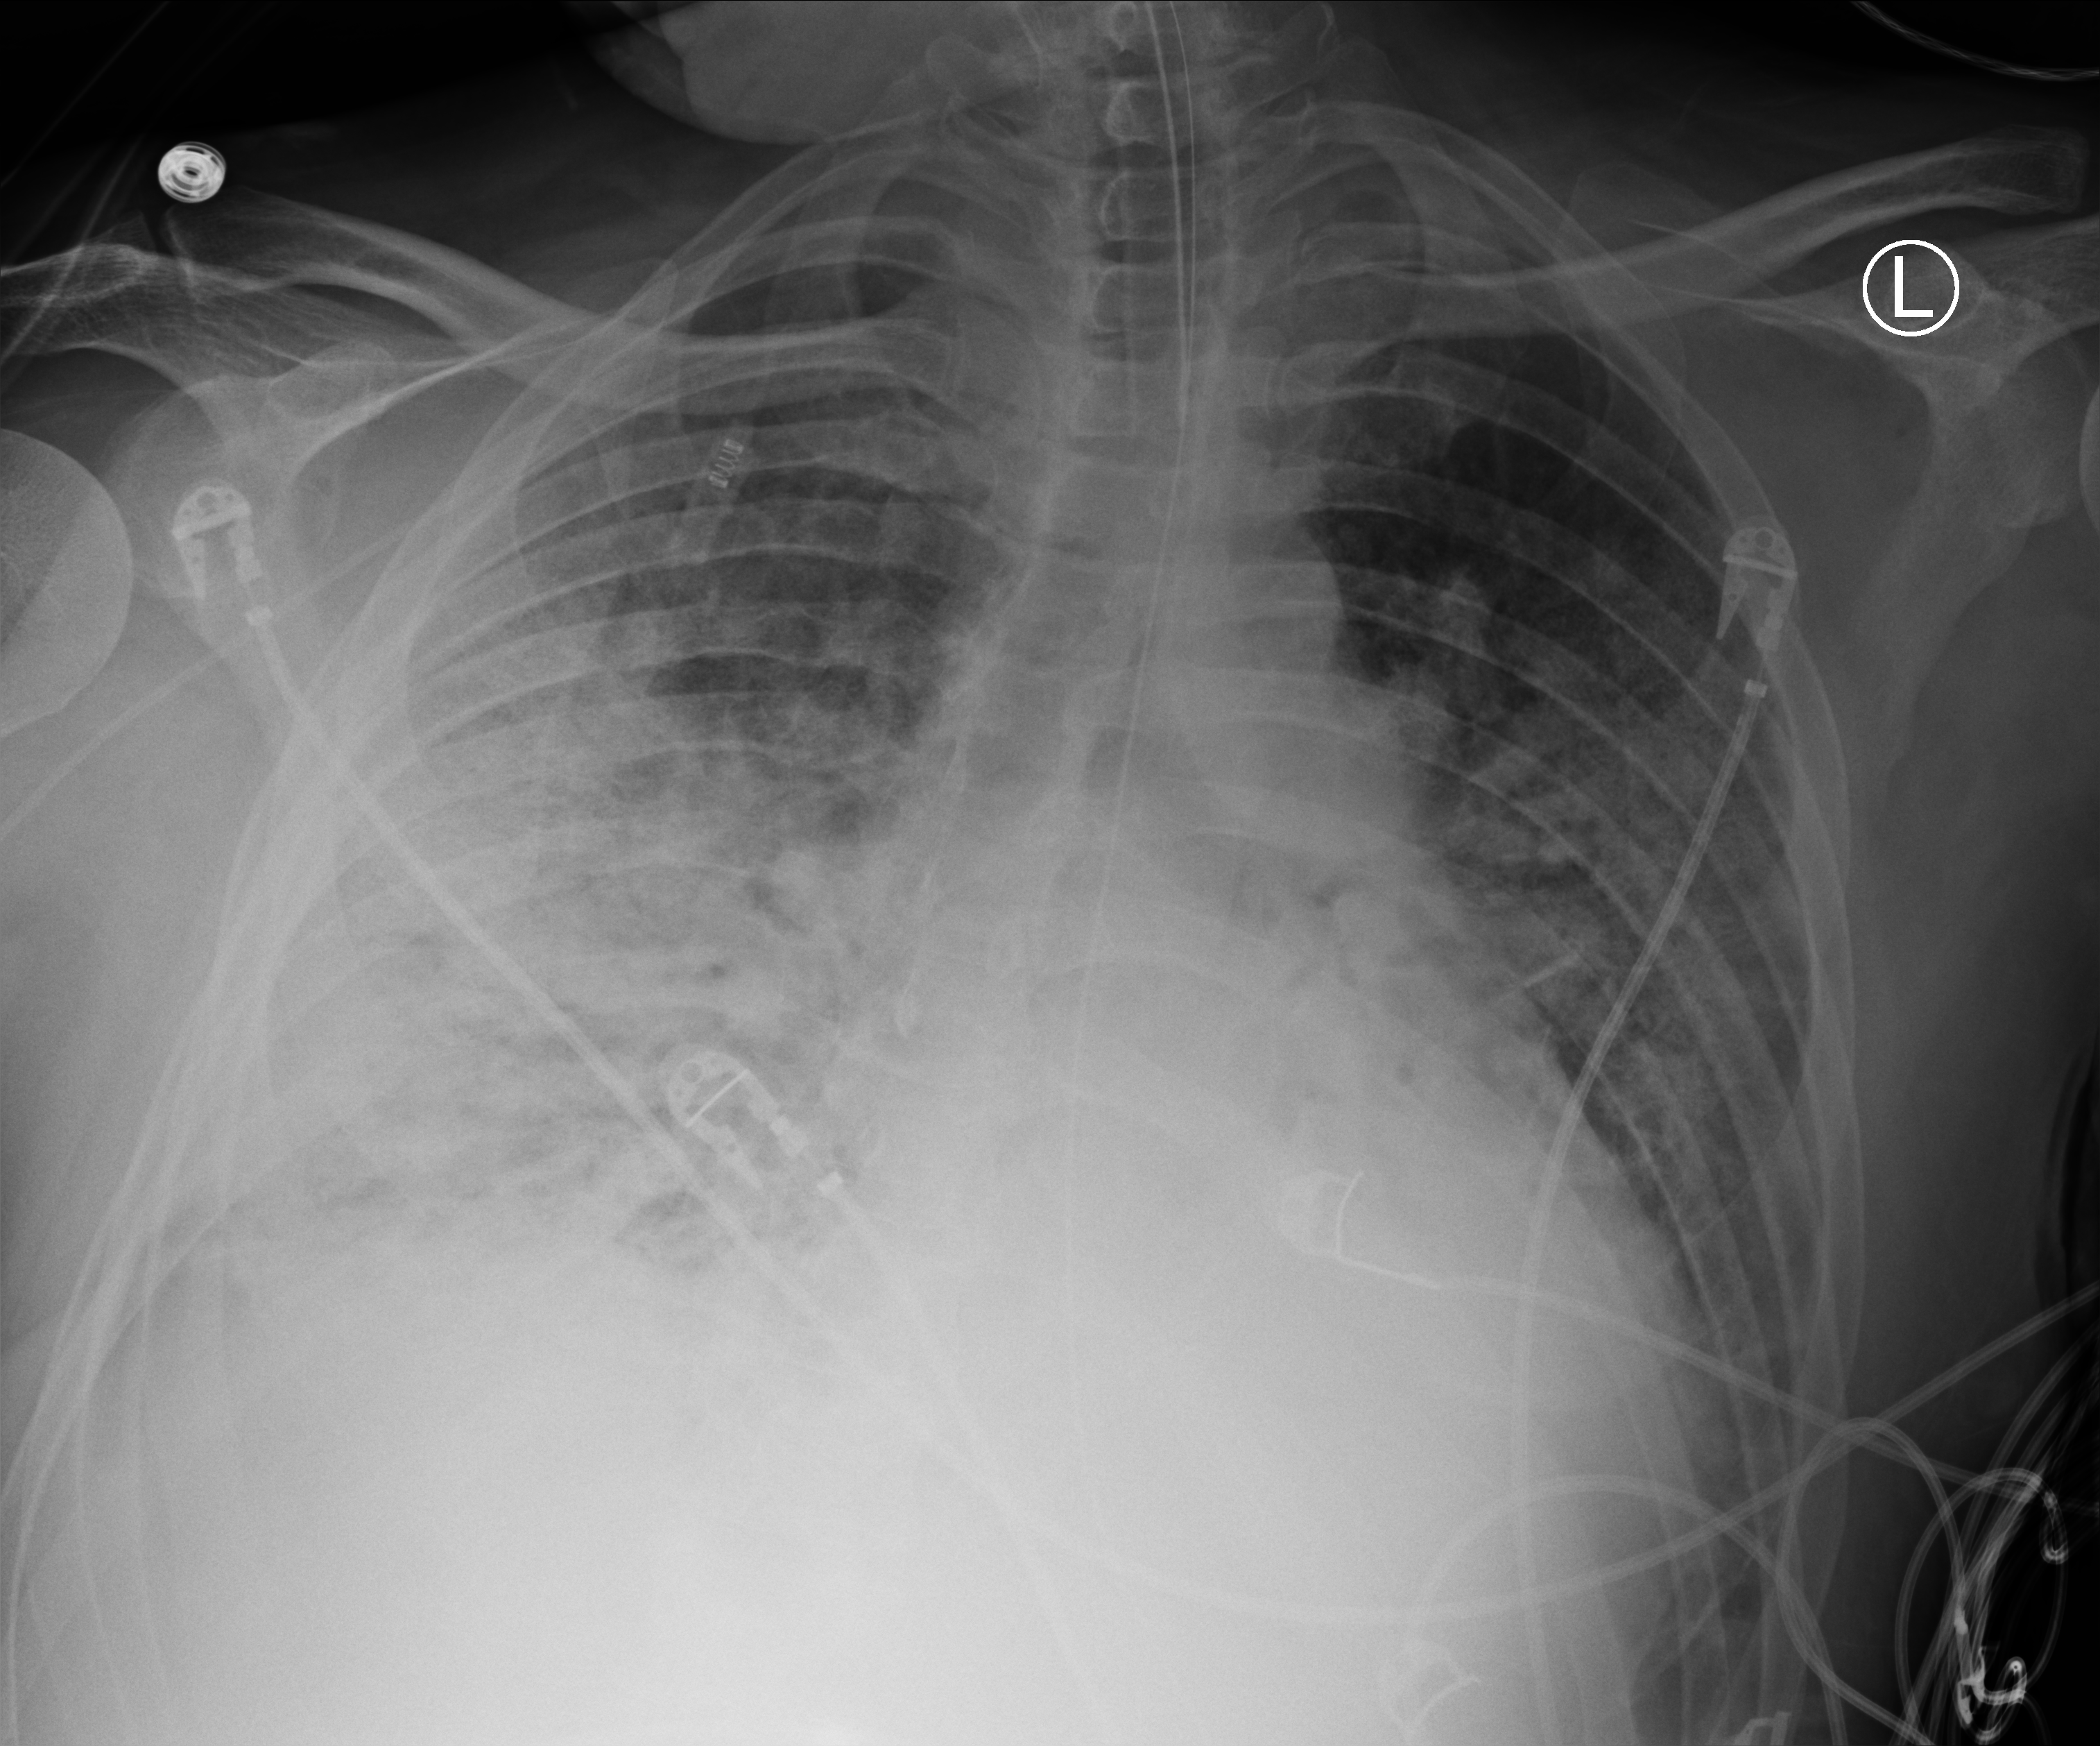
Bedside chest radiograph (computed radiography), anteroposterior (AP) projection. Male patient hospitalised with COVID-19, age 18–59 years.
From the hospital-stay record, not from the radiograph (when in the stay this image was taken is not recorded): mechanically ventilated during this hospital stay: yes; admitted to intensive care during this hospital stay: yes.